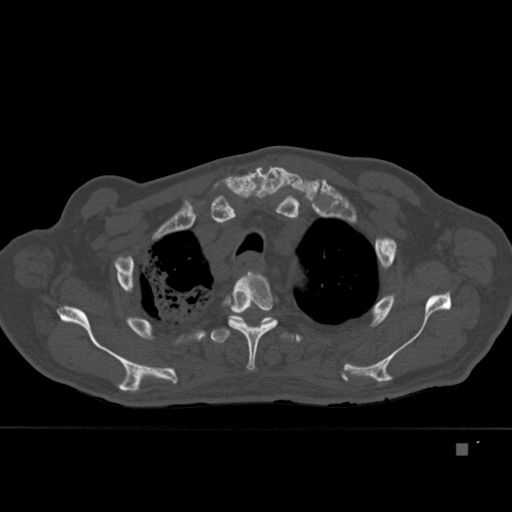
CT including the spine, one axial slice. Slice 332 of 451 in the series (ordered by position). Bone window (W 1800 / L 400 HU). 512 × 512 image matrix. Male patient, age 75 years. From the clinical record (not read from this slice): primary cancer: prostate.
Outlined on this slice (semi-automatic segmentation, software-assisted and operator-edited):
- T2 vertebra: box from (x=249, y=270) to (x=261, y=275) px
- T3 vertebra: (x=224, y=271)–(x=278, y=371)
- T4 vertebra: (x=210, y=315)–(x=294, y=344)